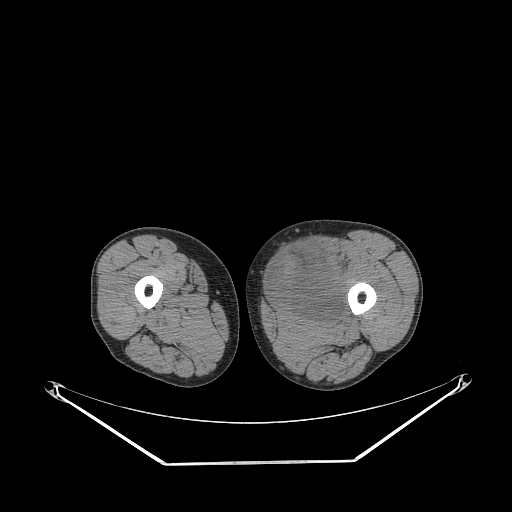
CT of an extremity soft-tissue mass (from a PET/CT study), one axial slice; position 237 of 267 along the scan axis; reconstruction kernel STANDARD; soft-tissue window (W 400 / L 40 HU); 3.75 mm slice thickness; 512 × 512 image matrix, field of view 500 × 500 mm. Male patient. From the clinical record (not read from this slice): histological type: pleiomorphic liposarcoma; grade: high; site of the primary tumour: left thigh.
Structures marked on this image (expert contour drawn on MRI and transferred to this co-registered scan by the dataset authors):
- gross tumour volume including surrounding oedema: bounding box <267,240,353,320> (left, top, right, bottom; pixels)
- gross tumour volume (mass): <269,244,344,320>